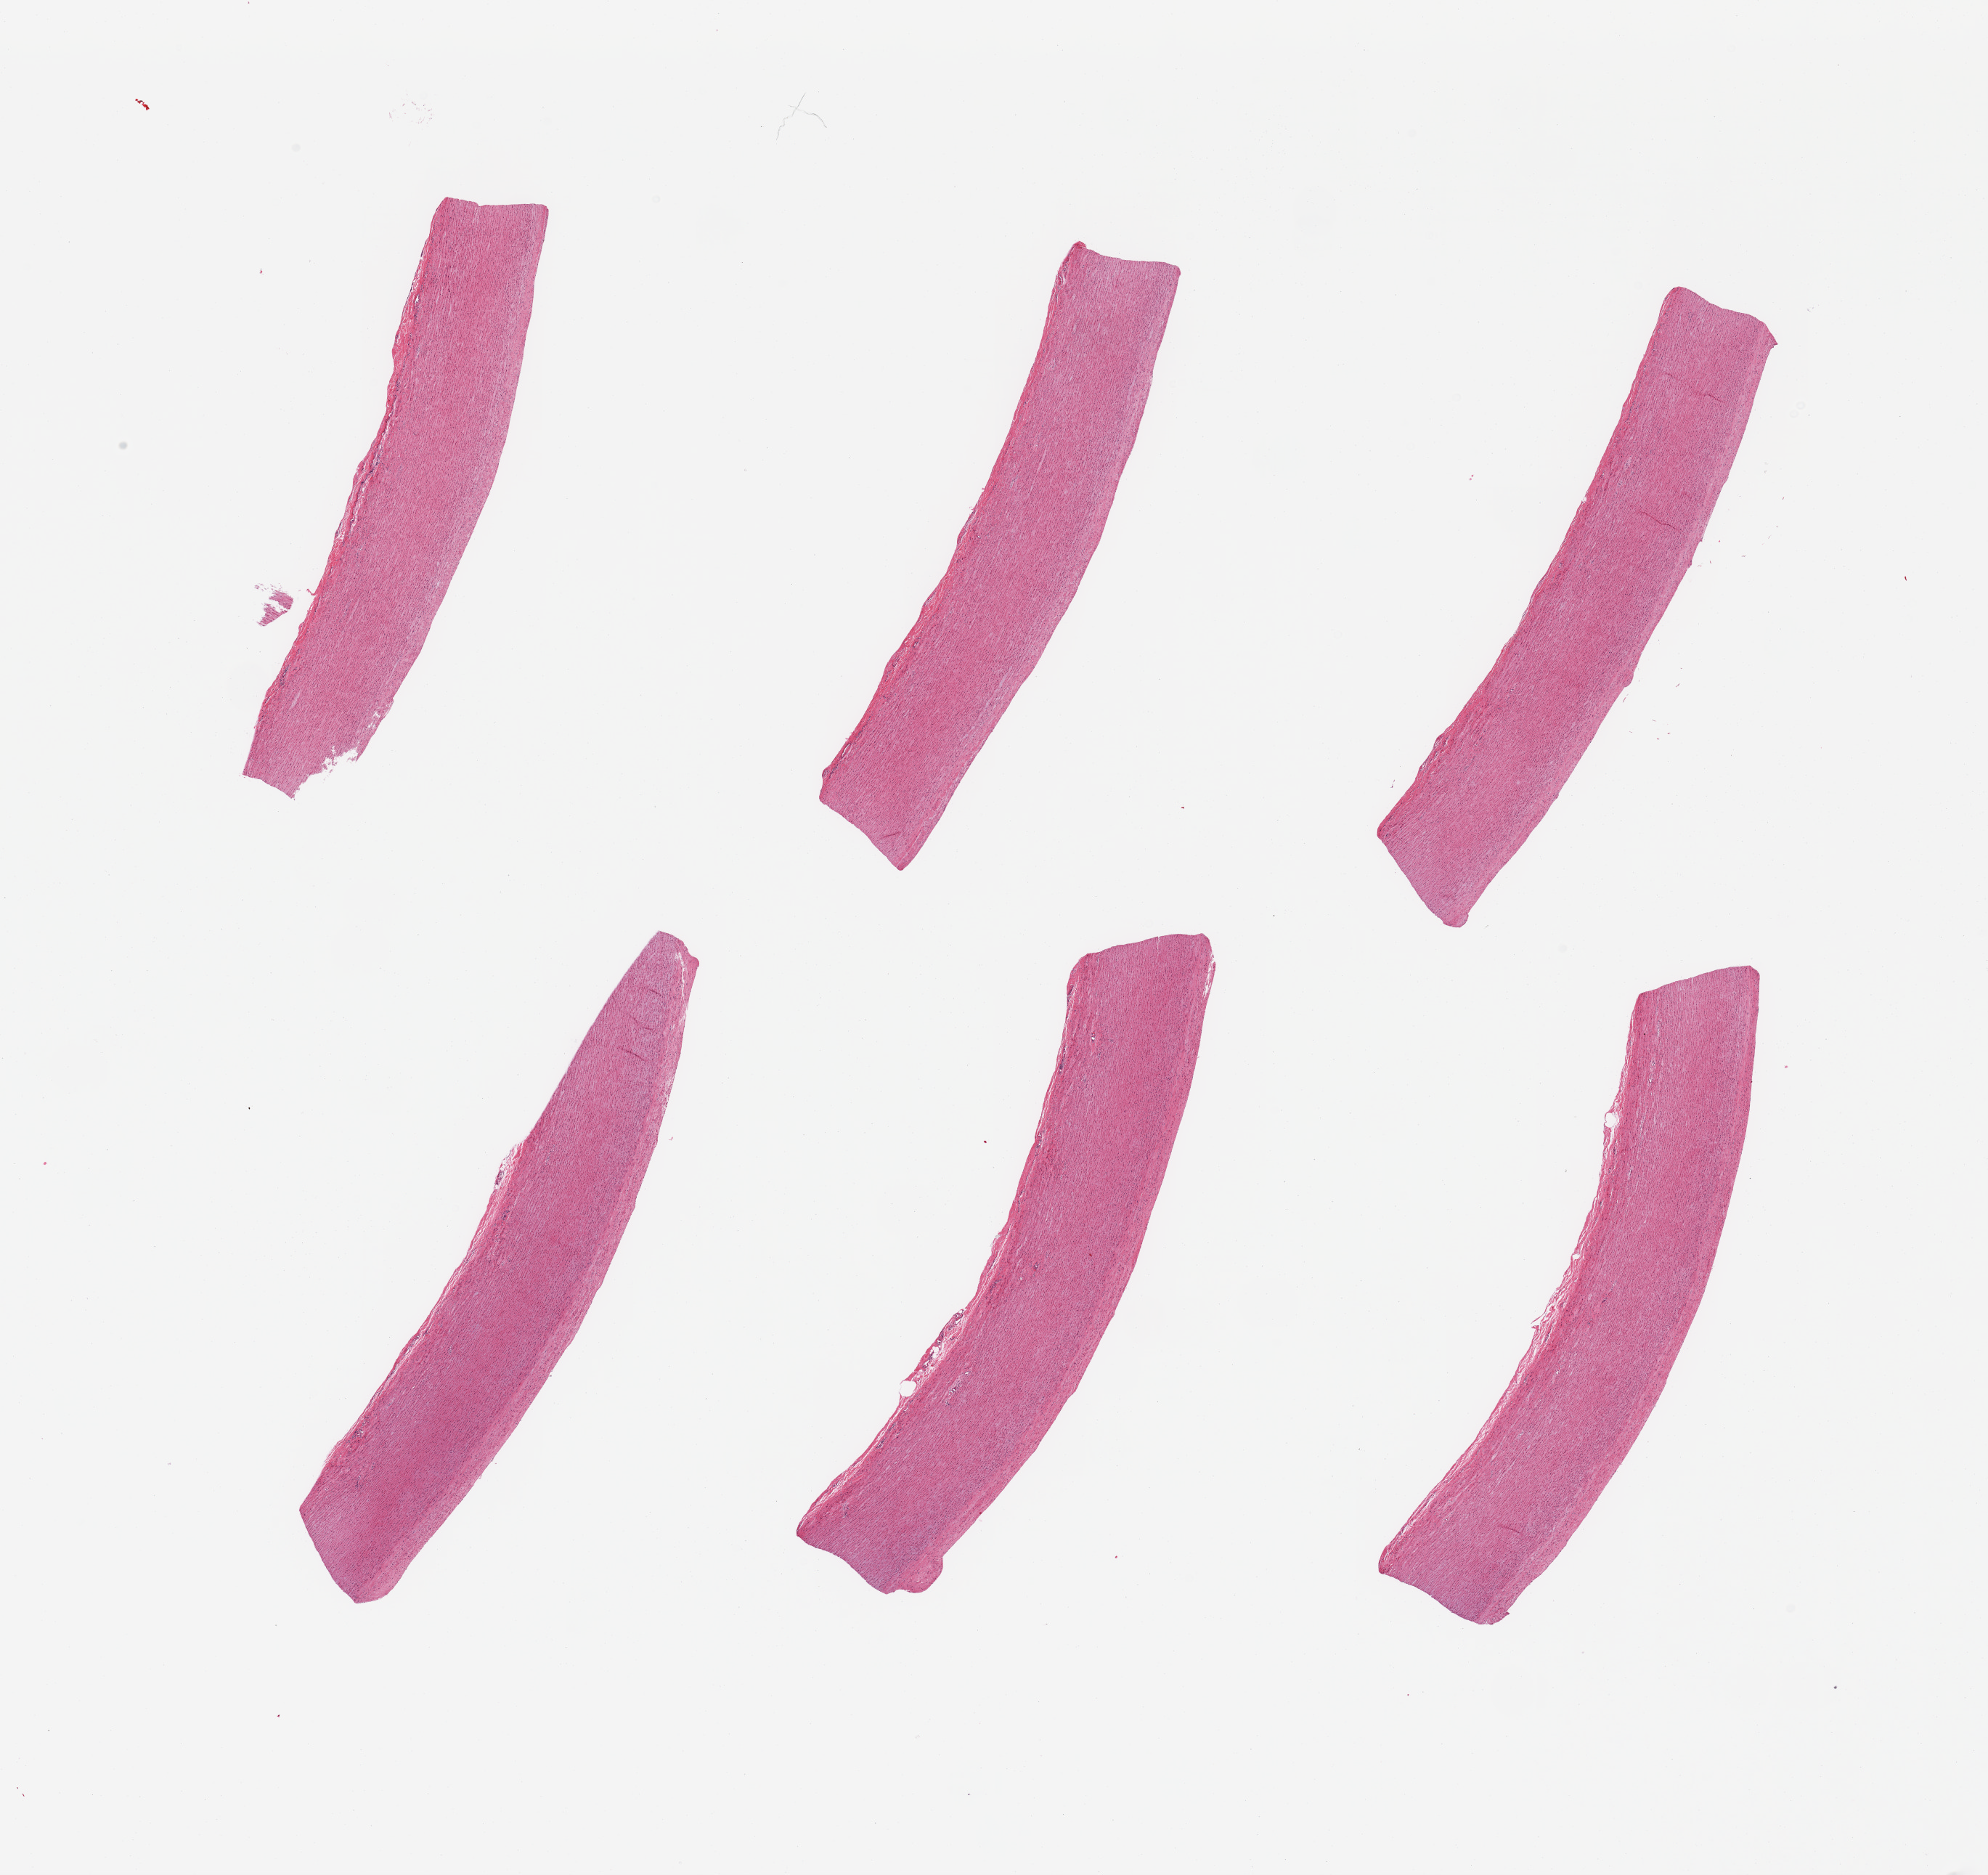
Whole-slide image, hematoxylin and eosin (H&E) stain, low-resolution overview of the scanned area, about 21.7 x 20.4 mm (from a 20x scan). PAXgene-fixed paraffin-embedded (PFPE) section. Target tissue: aorta. Tissue donor sample.
Reviewer comment on this tissue sample: 6 pieces; no plaques, no lesions; well trimmed.